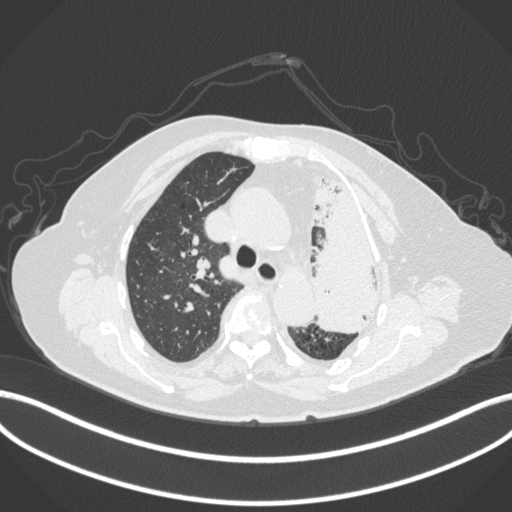
Chest CT, one axial slice. Position 282 of 399 along the scan axis. 120 kVp. Lung window (W 1500 / L -600 HU). 1 mm slice thickness. 512 × 512 image matrix. Female patient, age 75 years. From the clinical record (not read from this slice): clinical TNM (as recorded): T3 N3 M1.
Structures marked on this image (bounding box drawn by a radiologist):
- lung tumour (recorded histology: adenocarcinoma): bounding box [x1, y1, x2, y2] px = [301, 166, 393, 342]